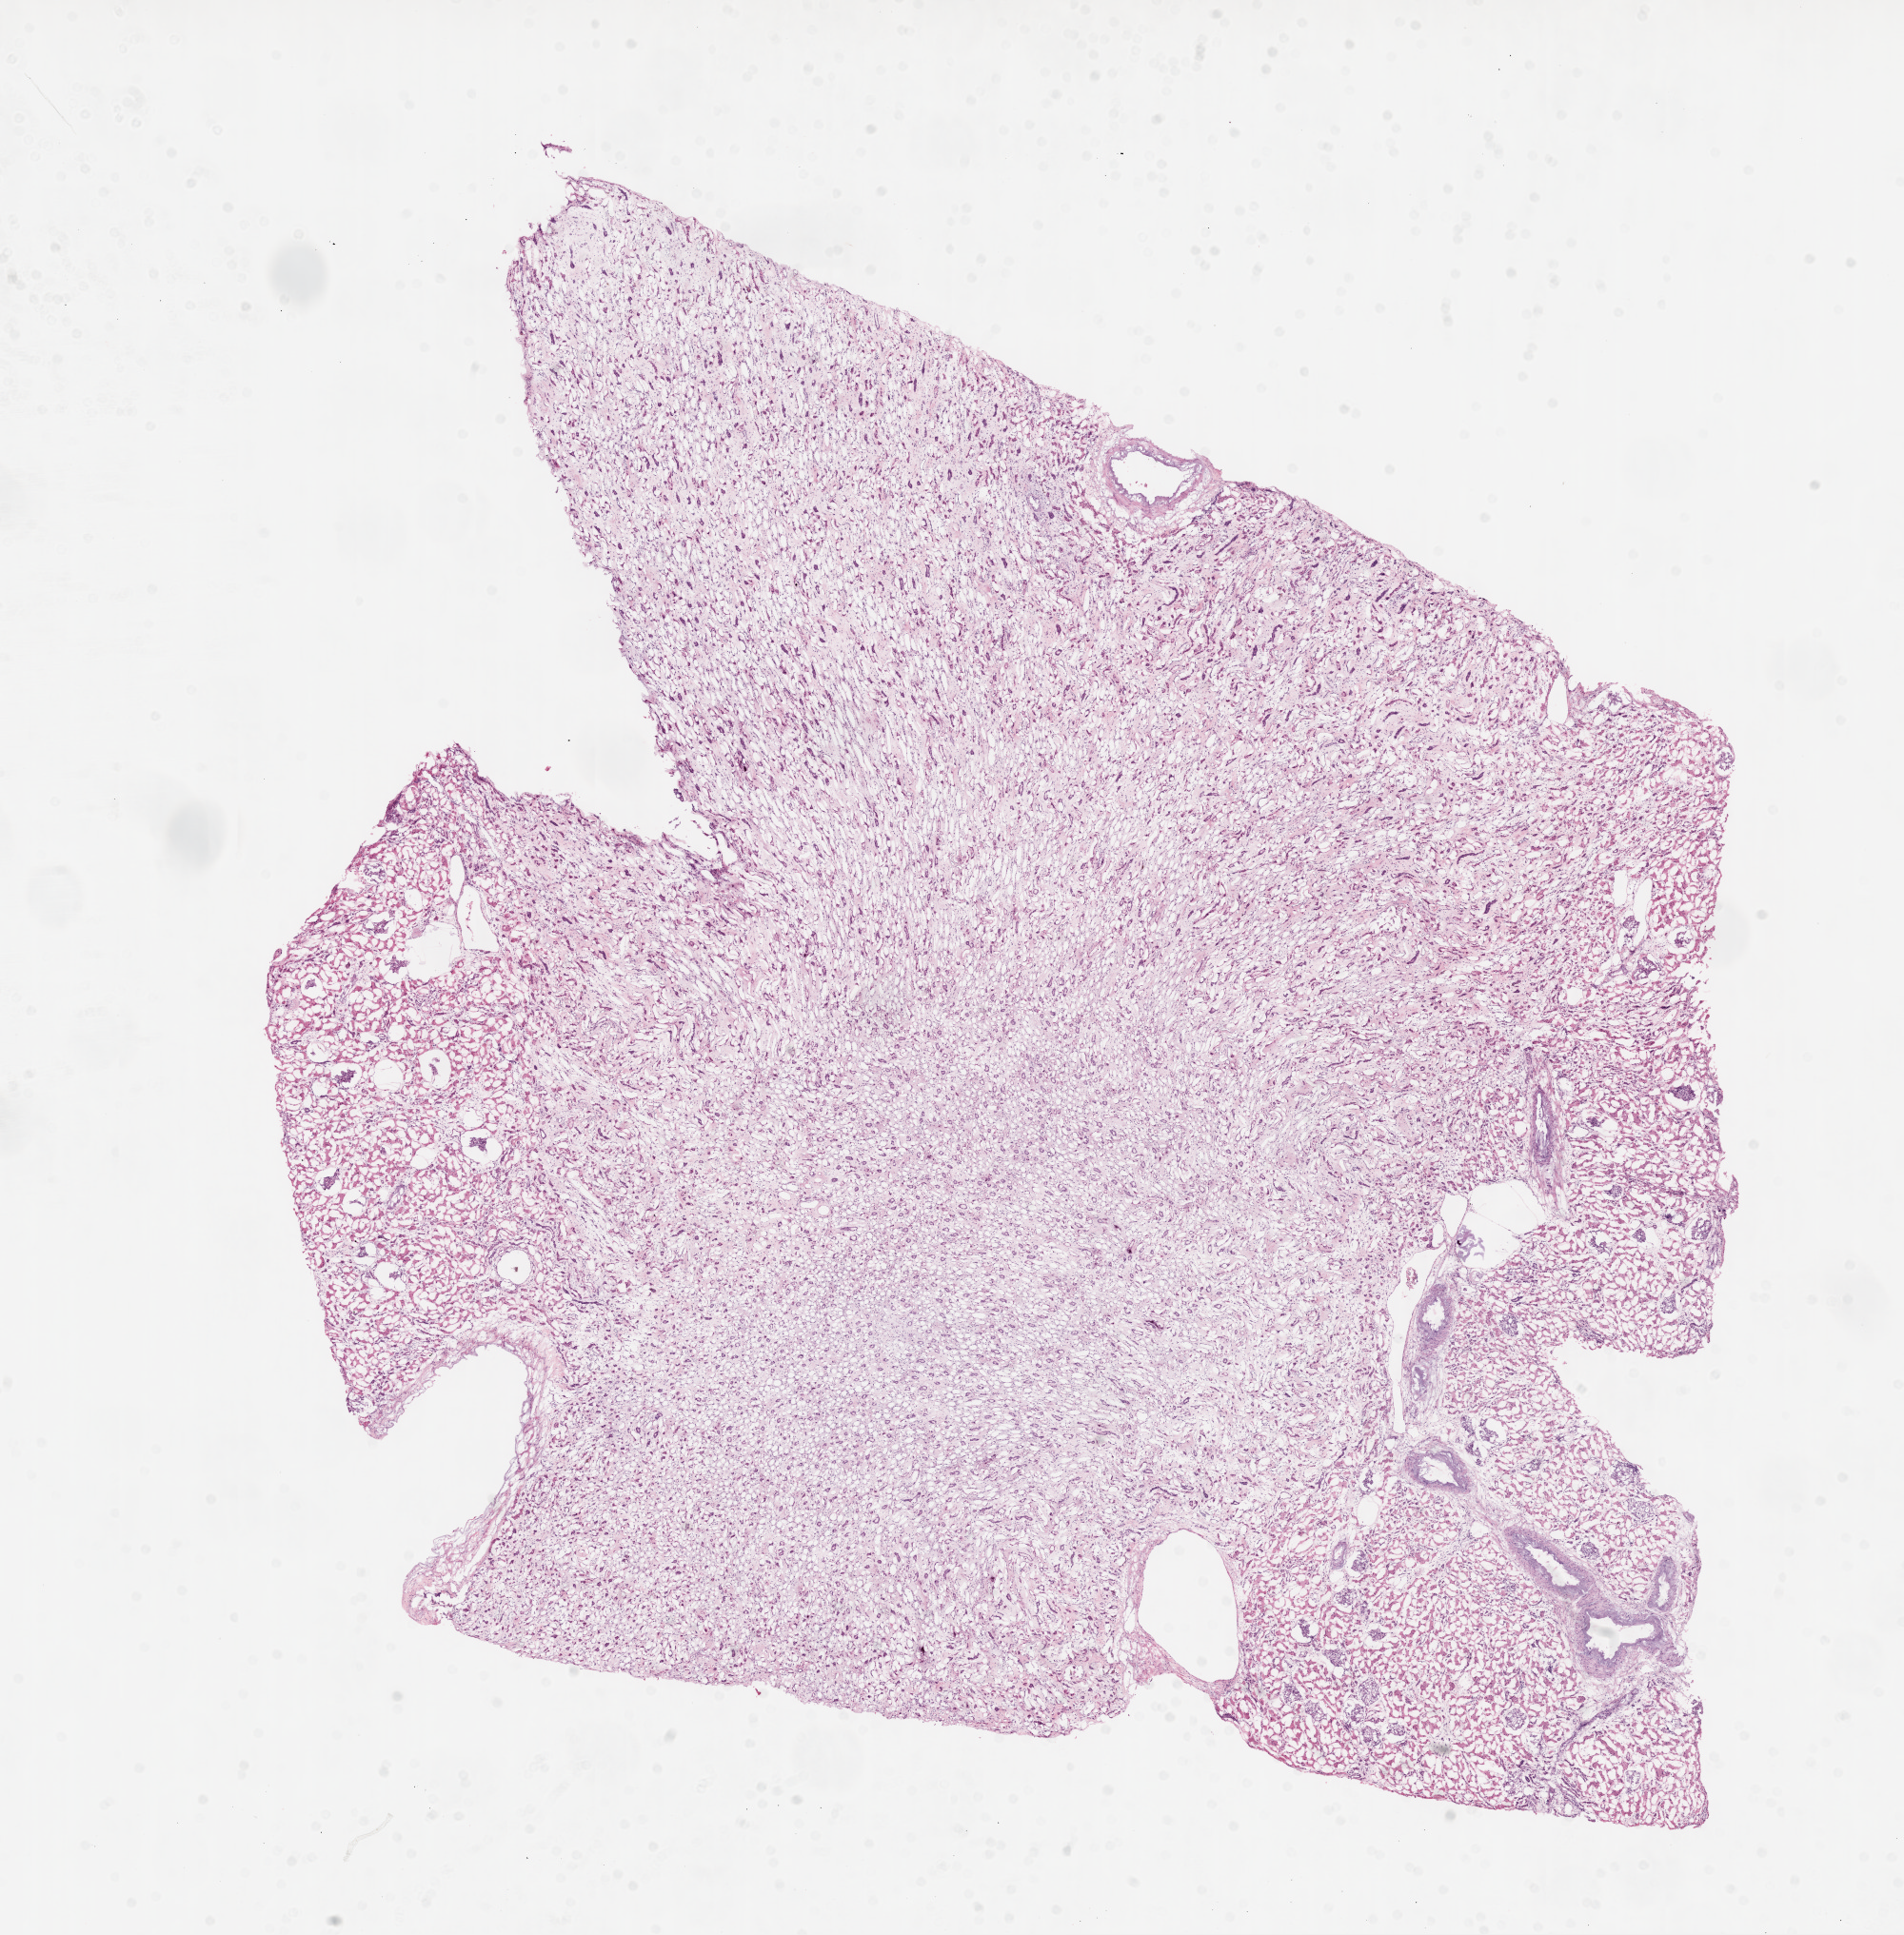
Digitized H&E tissue section (whole slide), a low-resolution overview of the entire scanned area, about 16.0 x 16.3 mm (slide scanned at 20x); frozen section from the top of the tissue portion; kidney, solid tissue normal (non-tumour tissue) sample. Male patient; age at initial diagnosis 82 years.
- this section: solid tissue normal sample (biorepository sample class)
- patient diagnosis: Clear cell adenocarcinoma, NOS